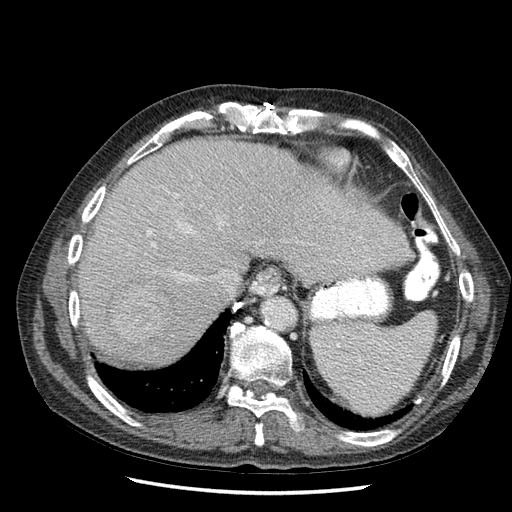
Contrast-enhanced abdominal CT (liver protocol), one axial slice. Slice 47 of 67 in the series (ordered by position). Reconstruction kernel STANDARD. Soft-tissue window (W 400 / L 40 HU). 2.5 mm slice thickness. 512 × 512 image matrix, field of view 360 × 360 mm. From the clinical record (not read from this slice): diagnosis: hepatocellular carcinoma (patient treated with transarterial chemoembolisation; whether this scan precedes or follows treatment is not stated here); TNM stage (as recorded): Stage-I; Child-Pugh class: A; tumour nodularity: uninodular.
Outlined on this slice (semi-automatic segmentation, software-assisted and operator-edited):
- liver parenchyma outside the tumour (the mass and vessels are separate outlines, so this box may not span the whole liver): bounding box <78,136,414,366> (left, top, right, bottom; pixels)
- mass: <109,286,171,343>
- liver vessels: <148,195,235,289>